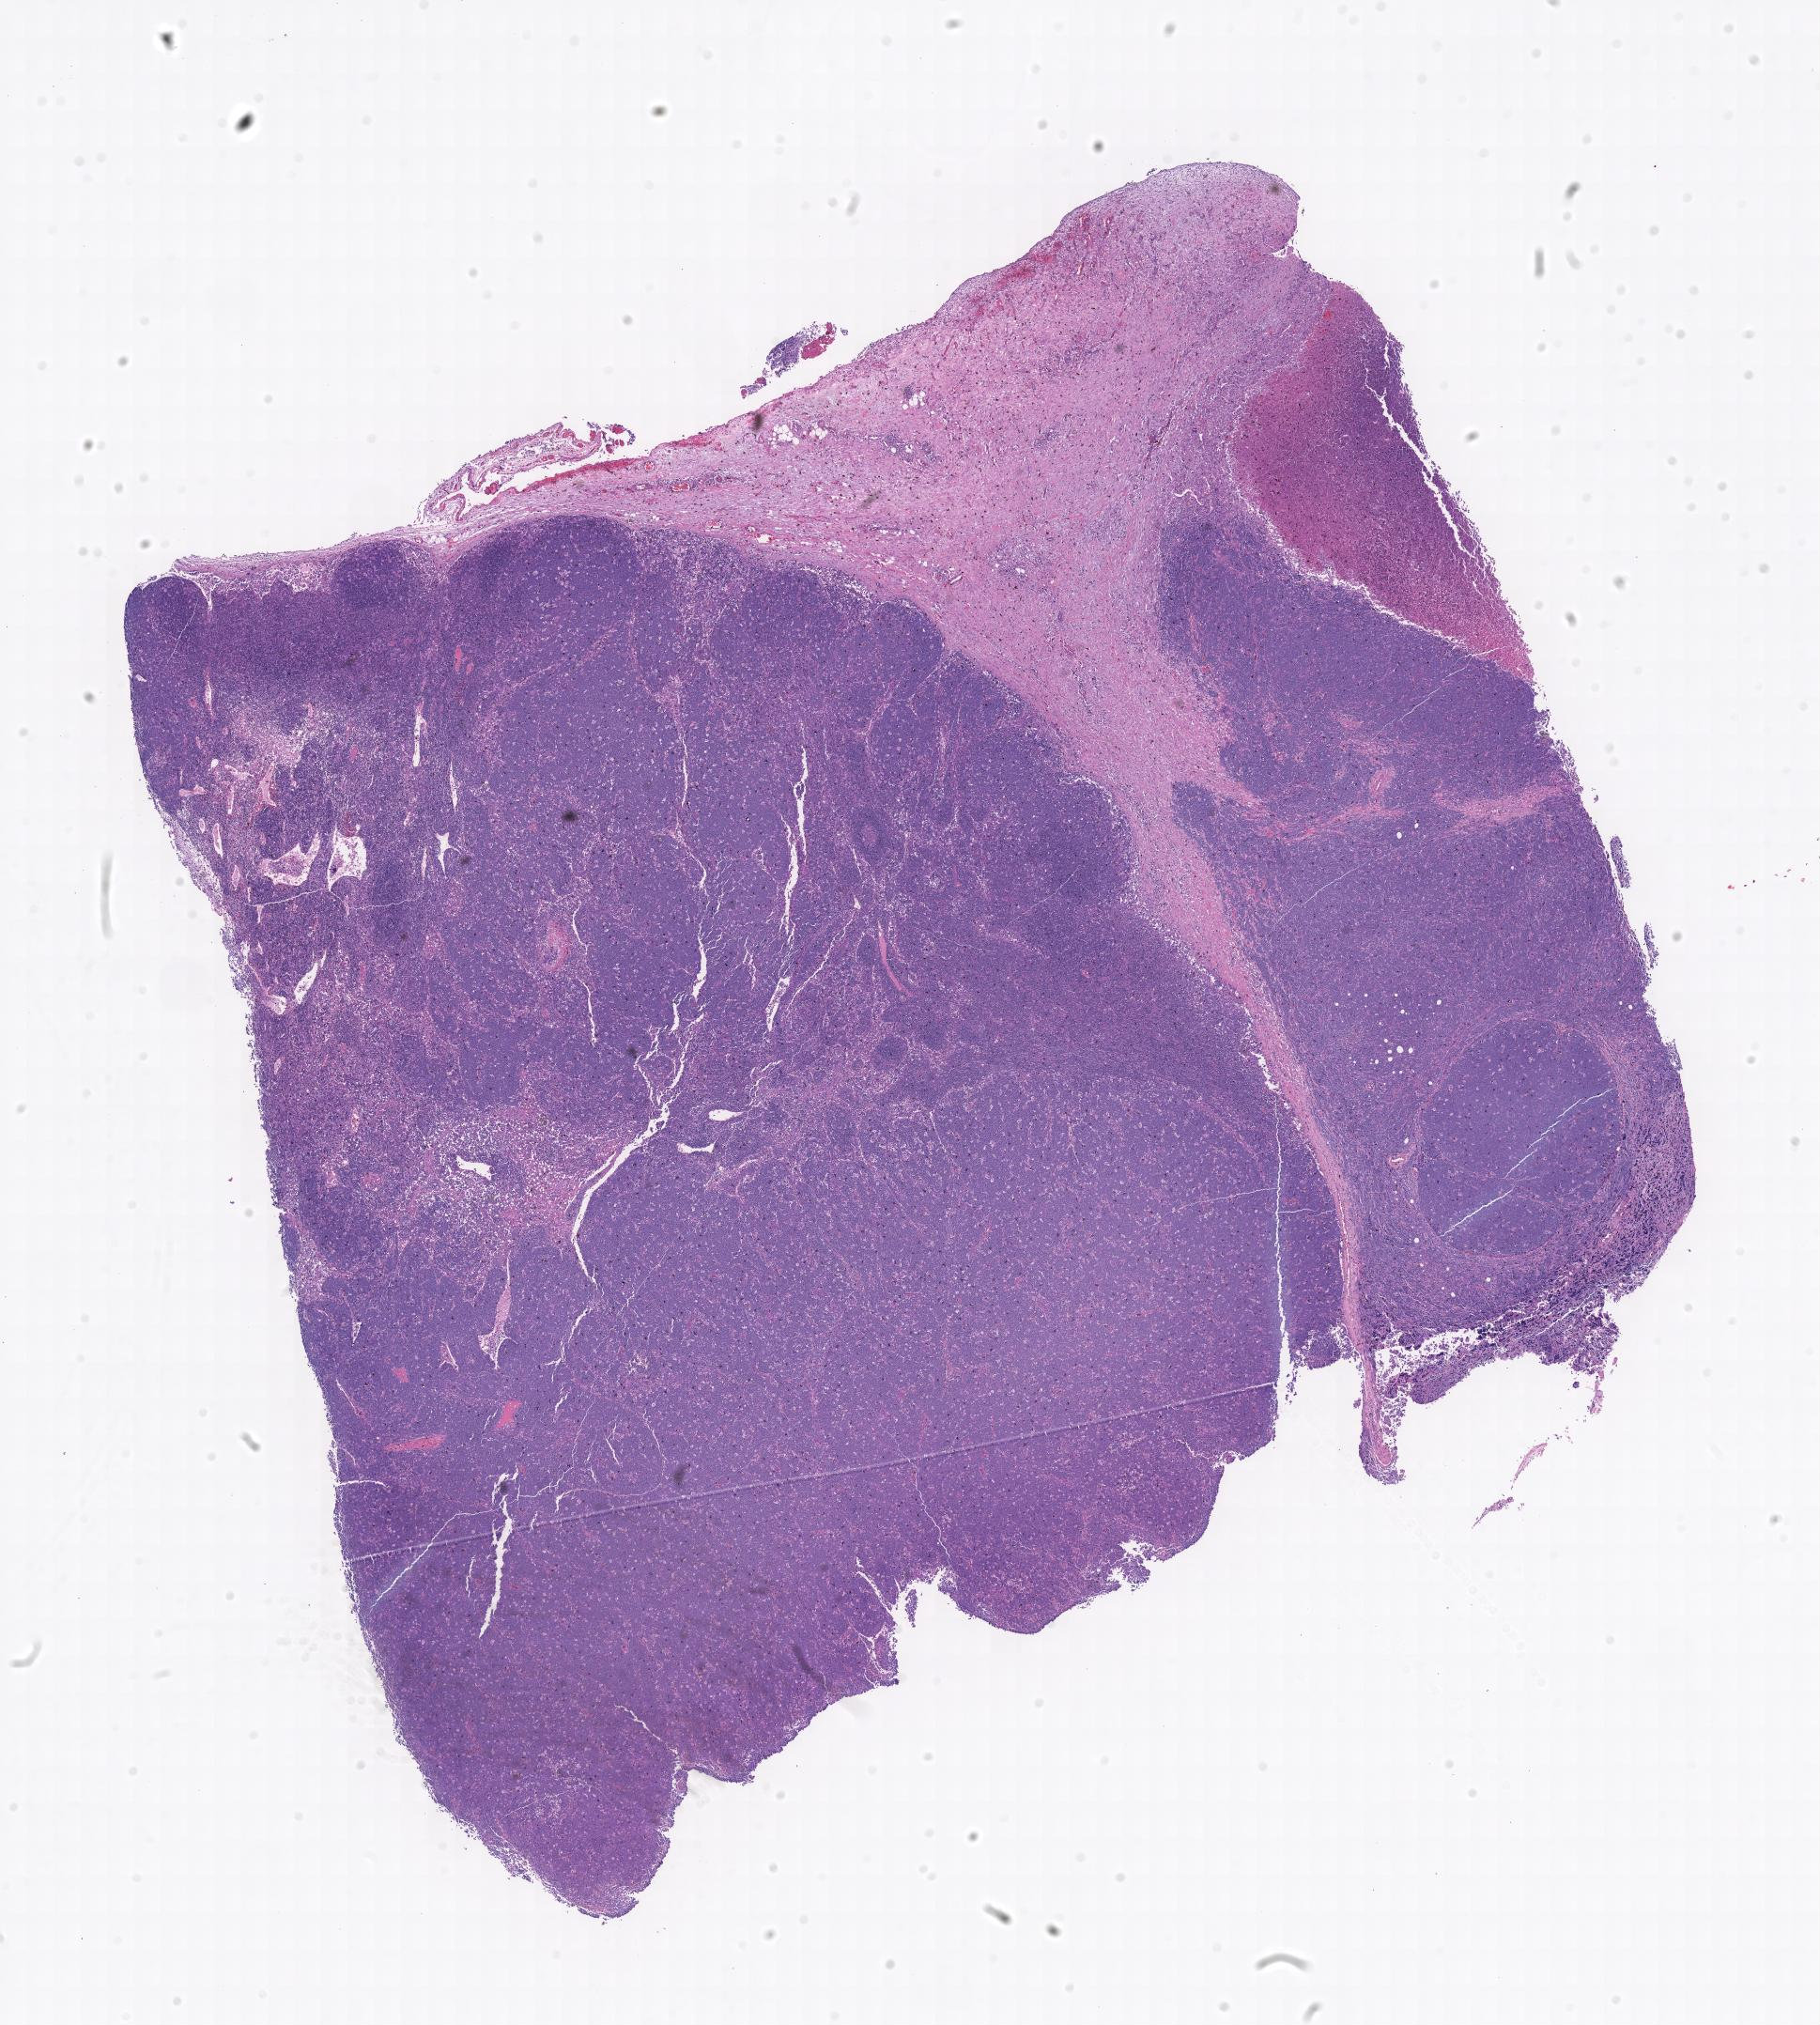
Digitized hematoxylin and eosin (H&E)-stained section, a low-resolution overview of the entire scanned area; specimen: tumor tissue; site: abdominal lymph node. Patient female; 14 years old.
* diagnosis: Burkitt lymphoma, NOS